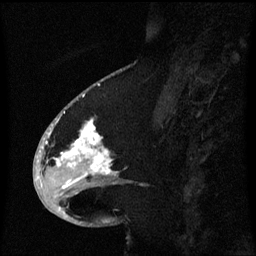
Breast MRI (dynamic contrast-enhanced), one sagittal slice. Position 27 of 60 along the scan axis. Dynamic contrast-enhanced series, image 2 of 3 at this slice position (ordered by acquisition). 1.5 T. TE 4.2 ms, TR 8.4 ms. 256 × 256 image matrix, field of view 200 × 200 mm. Female patient, age 53 years. Case-level facts recorded for this patient, not image findings: setting: breast cancer imaged before/during neoadjuvant chemotherapy; receptor status: HR-positive, HER2-negative.
Annotated regions visible in this slice (semi-automatic segmentation, software-assisted and operator-edited):
- analysis volume of interest (the breast-tissue region the enhancement analysis was run in; not a lesion): bounding box [x1, y1, x2, y2] px = [49, 108, 133, 201]
- tumour enhancement mask (voxels above the 70 % enhancement threshold inside the analysis volume of interest): [57, 120, 113, 175]